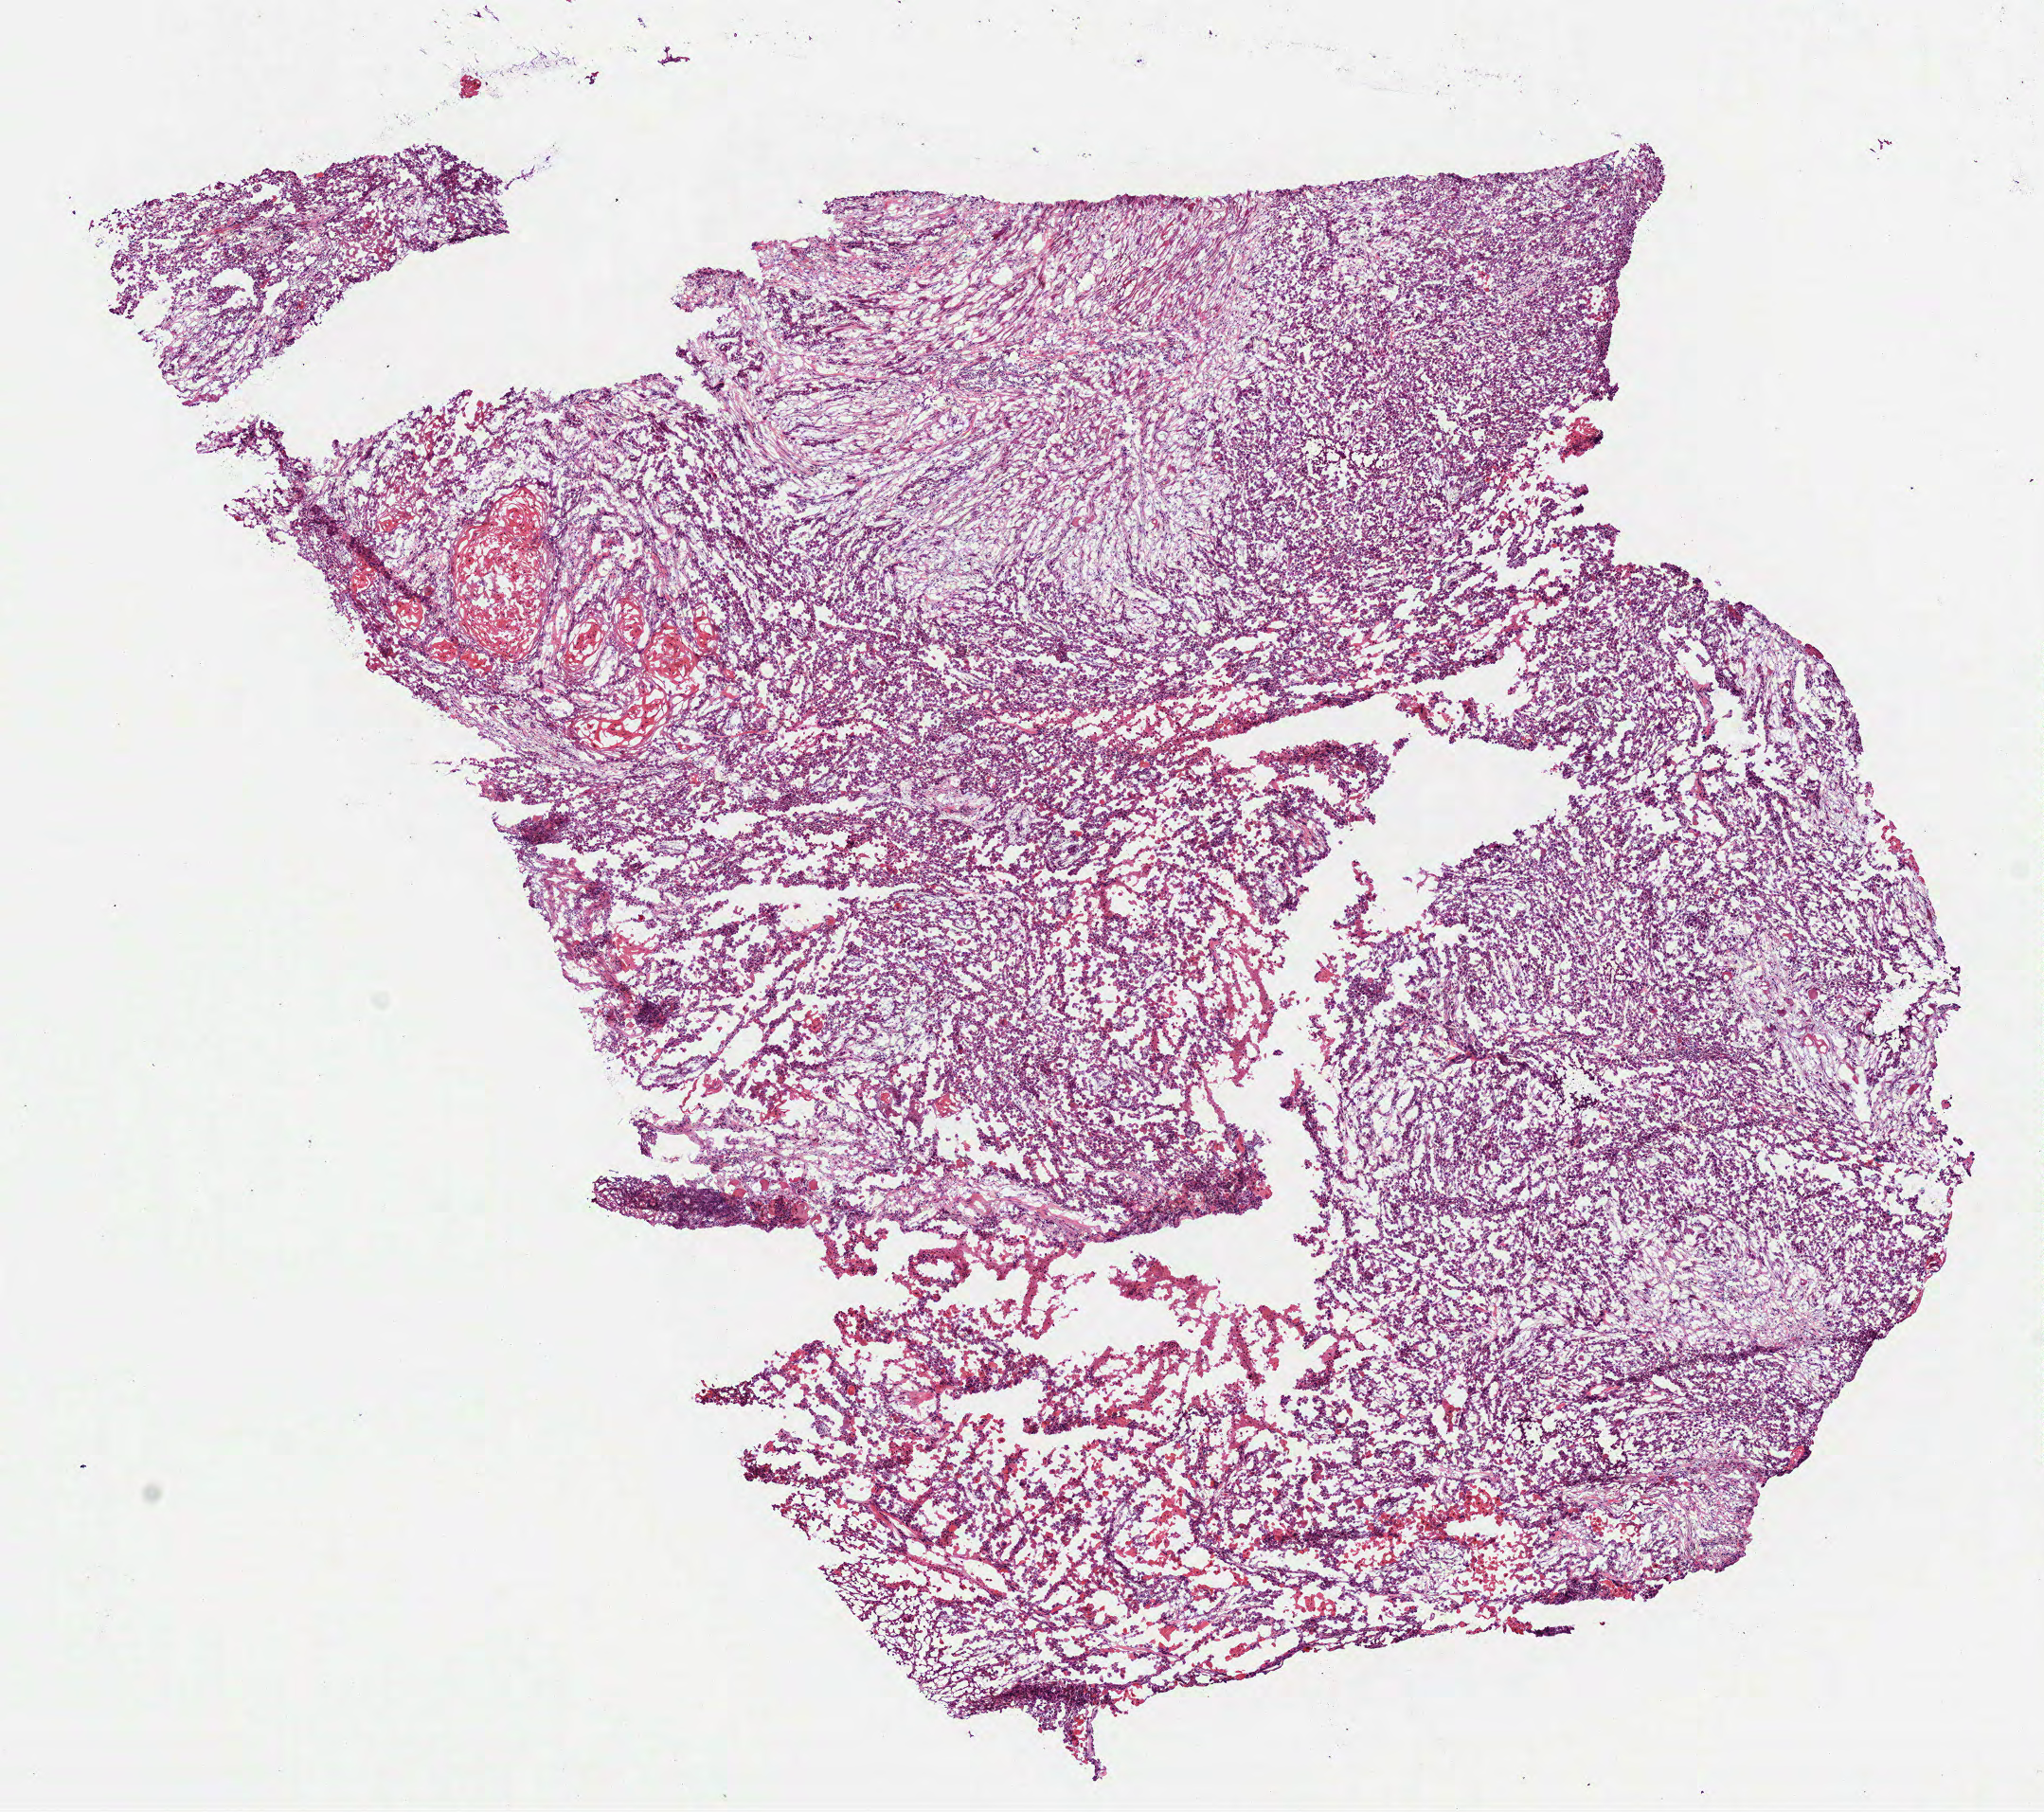
Digitized H&E-stained tissue section (whole slide), shown as a low-resolution overview of the whole scanned area (about 8.7 x 7.7 mm). Frozen section. Primary tumour sample from the head and neck. Female patient; age at initial diagnosis 48 years. Histologic grade: GX (grade cannot be assessed). Composition of this section per pathologist review: tumour cells 75%, tumour nuclei 75%, normal cells 0%, stromal cells 15%, necrosis 10%.
* diagnosis: Squamous cell carcinoma, NOS (overlapping lesion of lip, oral cavity and pharynx)
* AJCC pathologic stage: IVA (7th edition)